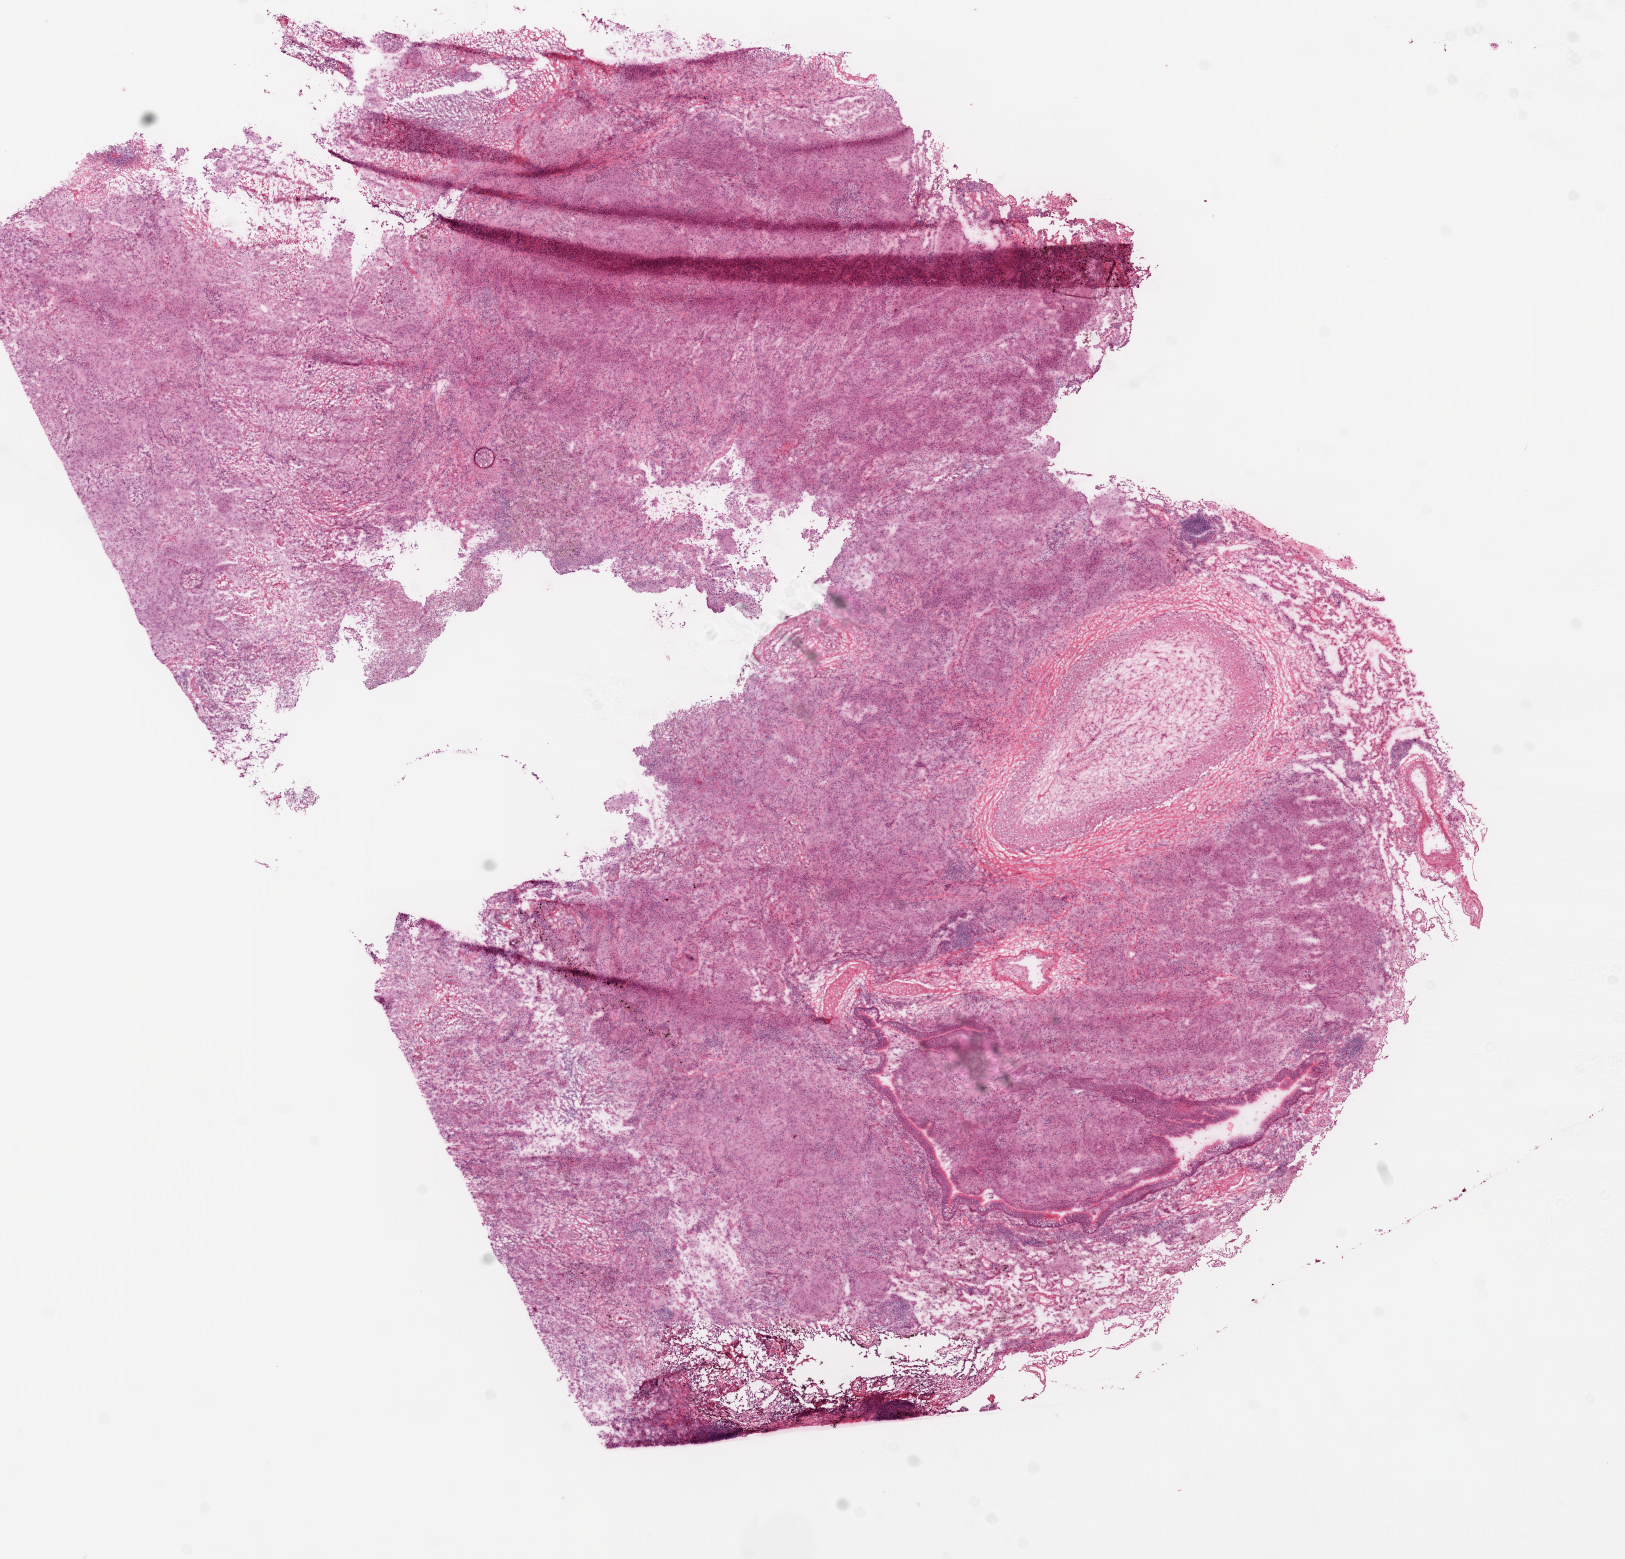
Digitized H&E tissue section (whole slide) — whole scanned area (about 13.0 x 12.5 mm, slide scanned at 20x) shown as a low-resolution overview; frozen section; lung, primary tumour sample. Female patient; age at initial diagnosis 69 years. Composition of this section per pathologist review: tumour cells 65%, tumour nuclei 70%, normal cells 5%, stromal cells 15%, necrosis 10%.
Histologic diagnosis: Squamous cell carcinoma, NOS (upper lobe, lung). TNM: T1b N0 M0. AJCC pathologic stage: IB. Laterality: left.